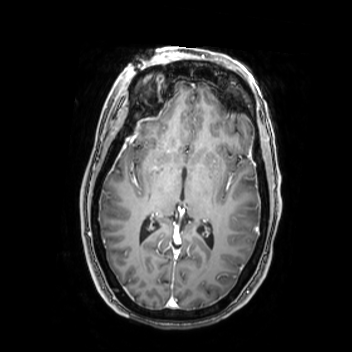
Brain MRI from a brain-tumour surgery series, one axial slice; slice 144 of 350 in the series (ordered by position); T1-weighted post-contrast; 0.9 mm slice thickness; 352 × 352 image matrix, field of view 280 × 280 mm. From the clinical record (not read from this slice): histopathology: Oligodendroglioma; WHO grade: 2; IDH mutation: yes.
Annotated regions visible in this slice (outlined manually by an expert reader):
- tumour: bounding box [x1, y1, x2, y2] px = [231, 183, 254, 223]